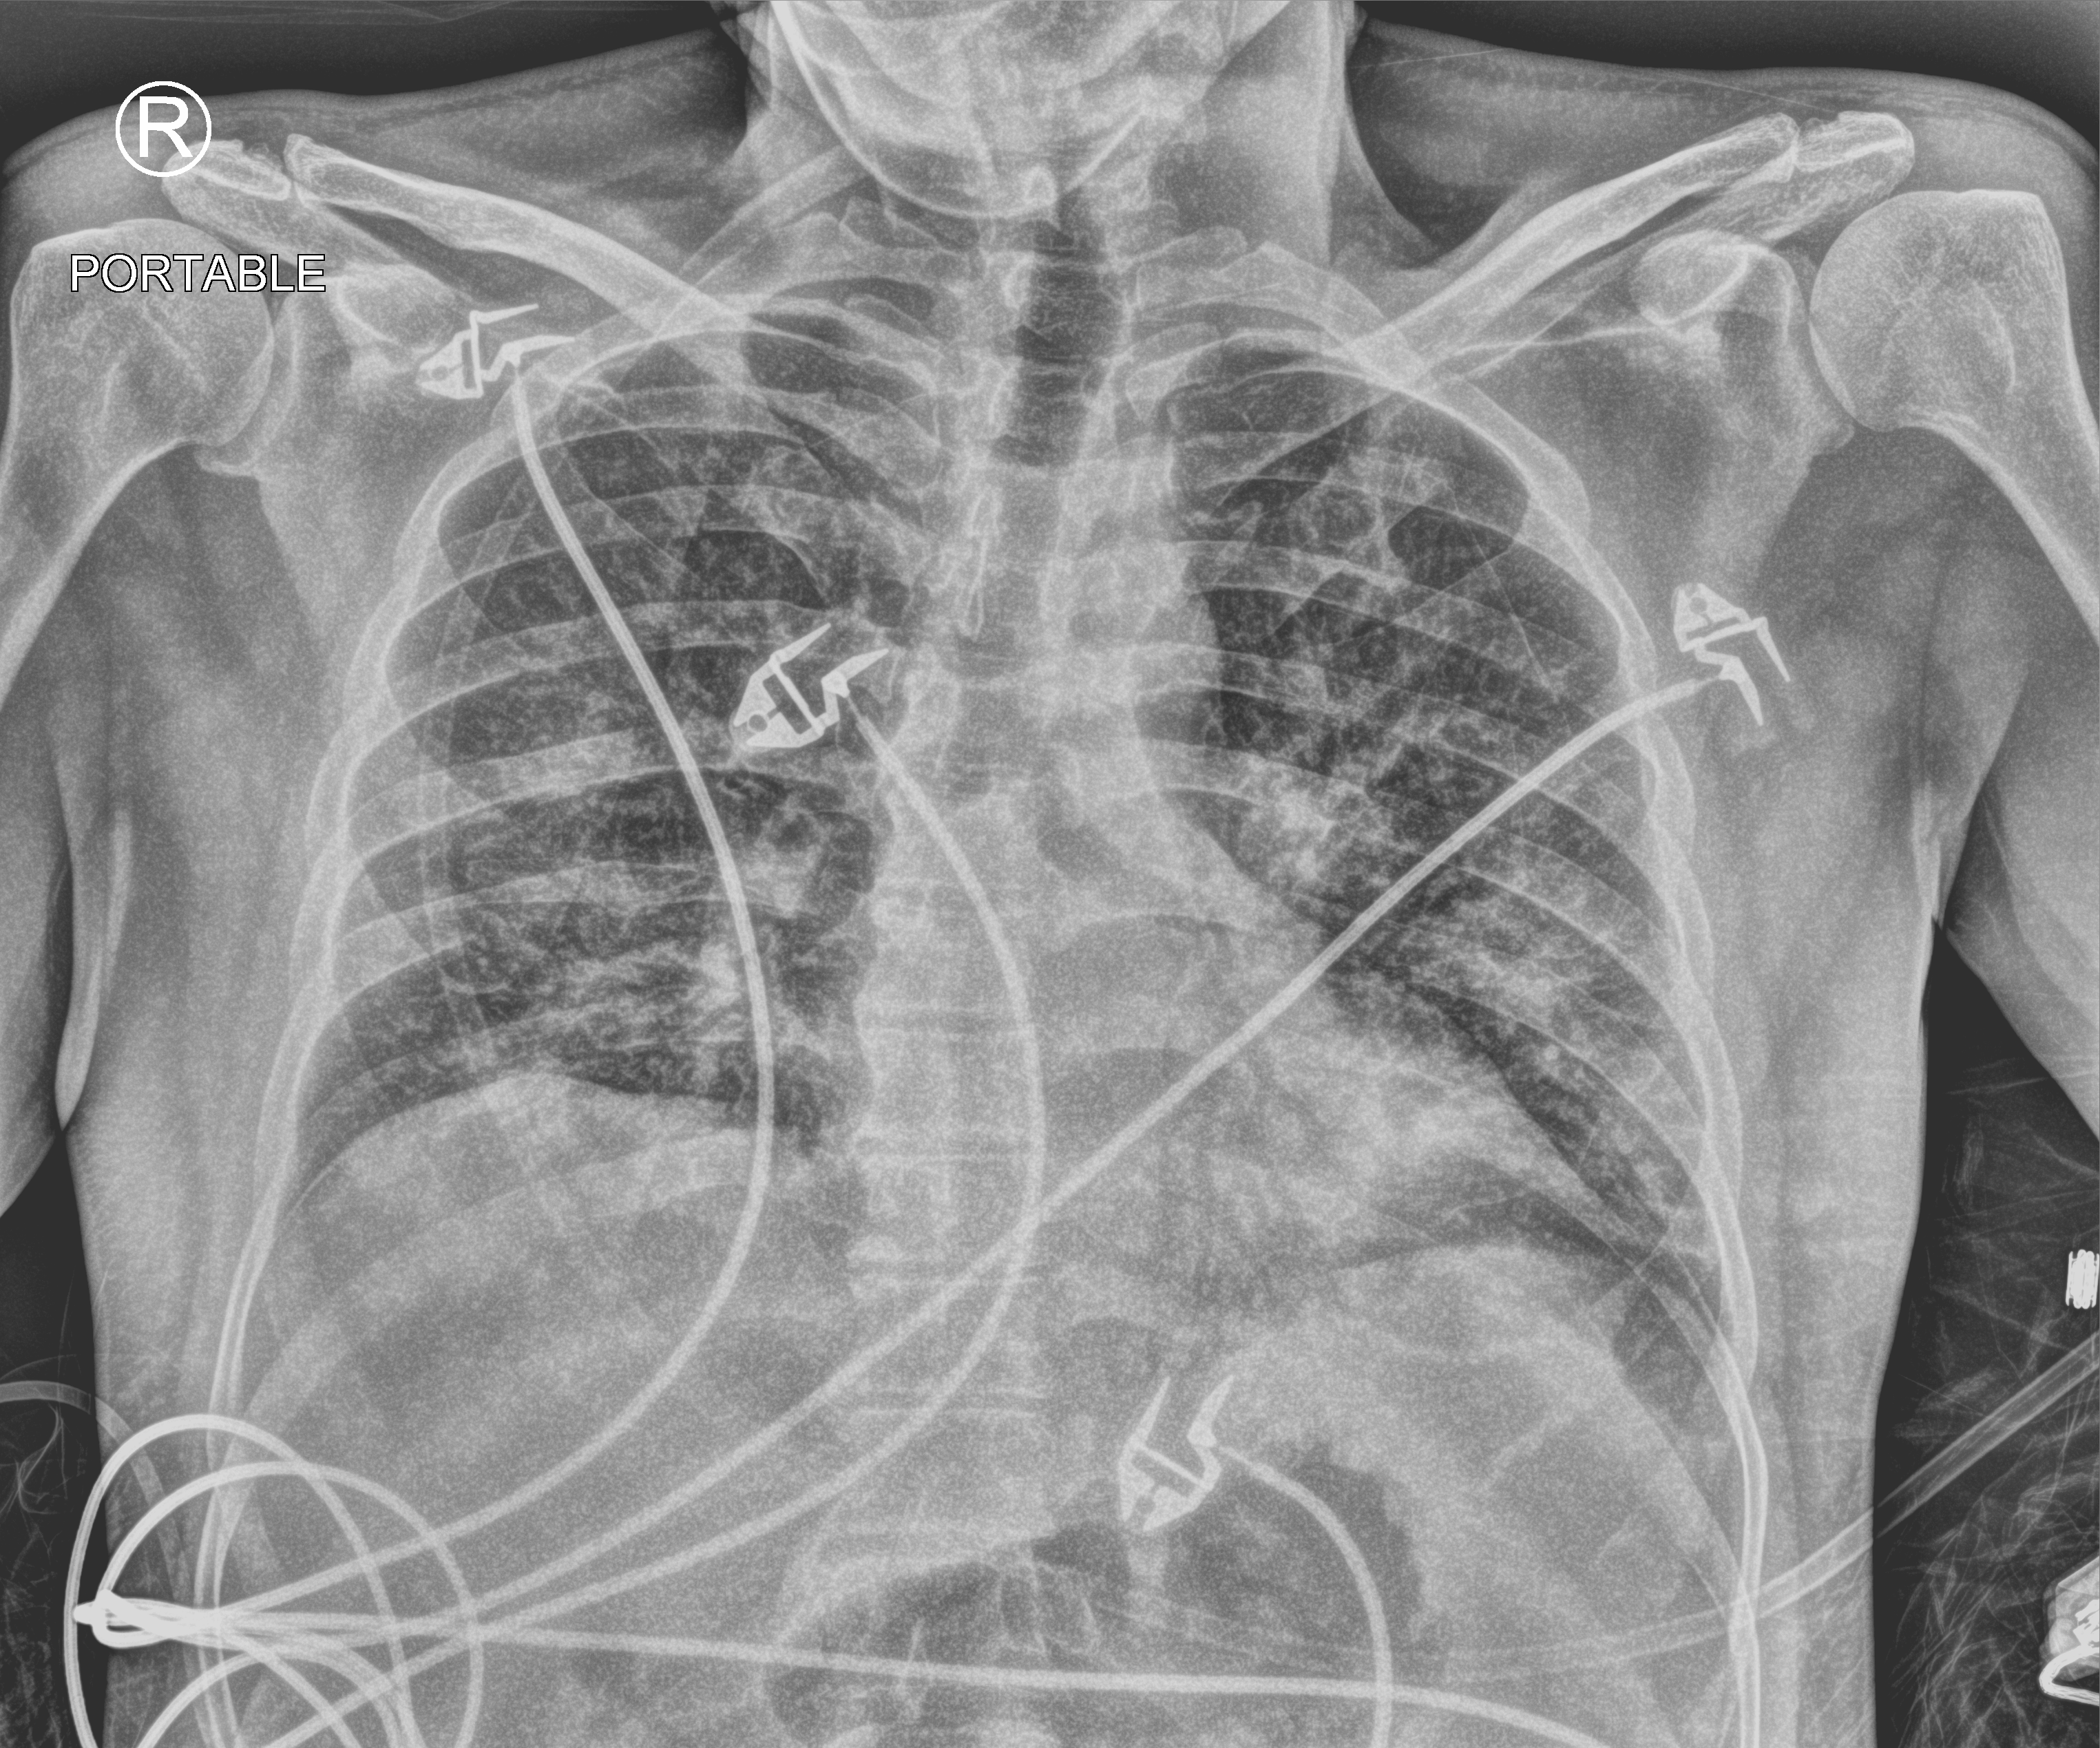
Bedside chest radiograph (computed radiography). Male patient hospitalised with COVID-19, age 18–59 years.
Admission-level facts for this patient (not findings on this image; timing relative to this image not recorded): admitted to intensive care during this hospital stay: no; diabetes (admission record): no.